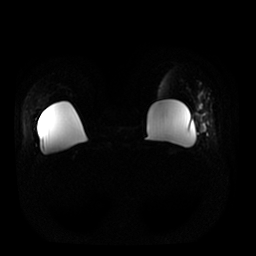
Breast MRI, one axial slice. Slice 5 of 25 in the series (ordered by position). Diffusion-weighted series; image 2 of 4 stored at this slice position (different b-values; order by instance number). 1.5 T. 256 × 256 image matrix, field of view 380 × 380 mm. Female patient.
Structures marked on this image (outlined manually by an expert reader):
- tumour on diffusion-weighted imaging: bounding box (x1, y1, x2, y2) in pixels: (196, 103, 207, 138)